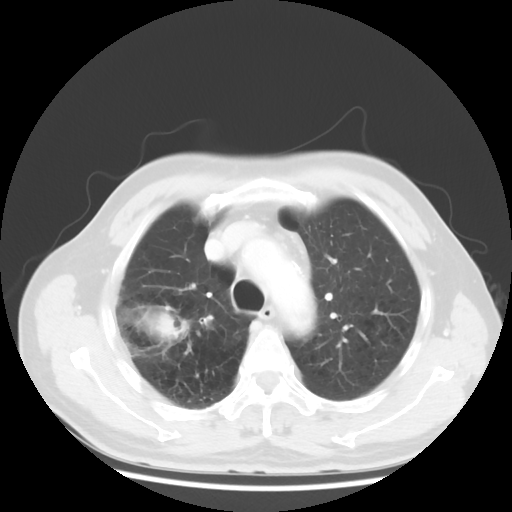
Chest CT, one axial slice; position 38 of 50 along the scan axis; 120 kVp; lung window (W 1500 / L -600 HU); 5 mm slice thickness; 512 × 512 image matrix. Patient: male, 69 years. From the clinical record (not read from this slice): clinical TNM (as recorded): T3 N0 M0.
Outlined on this slice (bounding box drawn by a radiologist):
- lung tumour (recorded histology: adenocarcinoma): bounding box [x1, y1, x2, y2] px = [112, 298, 198, 357]